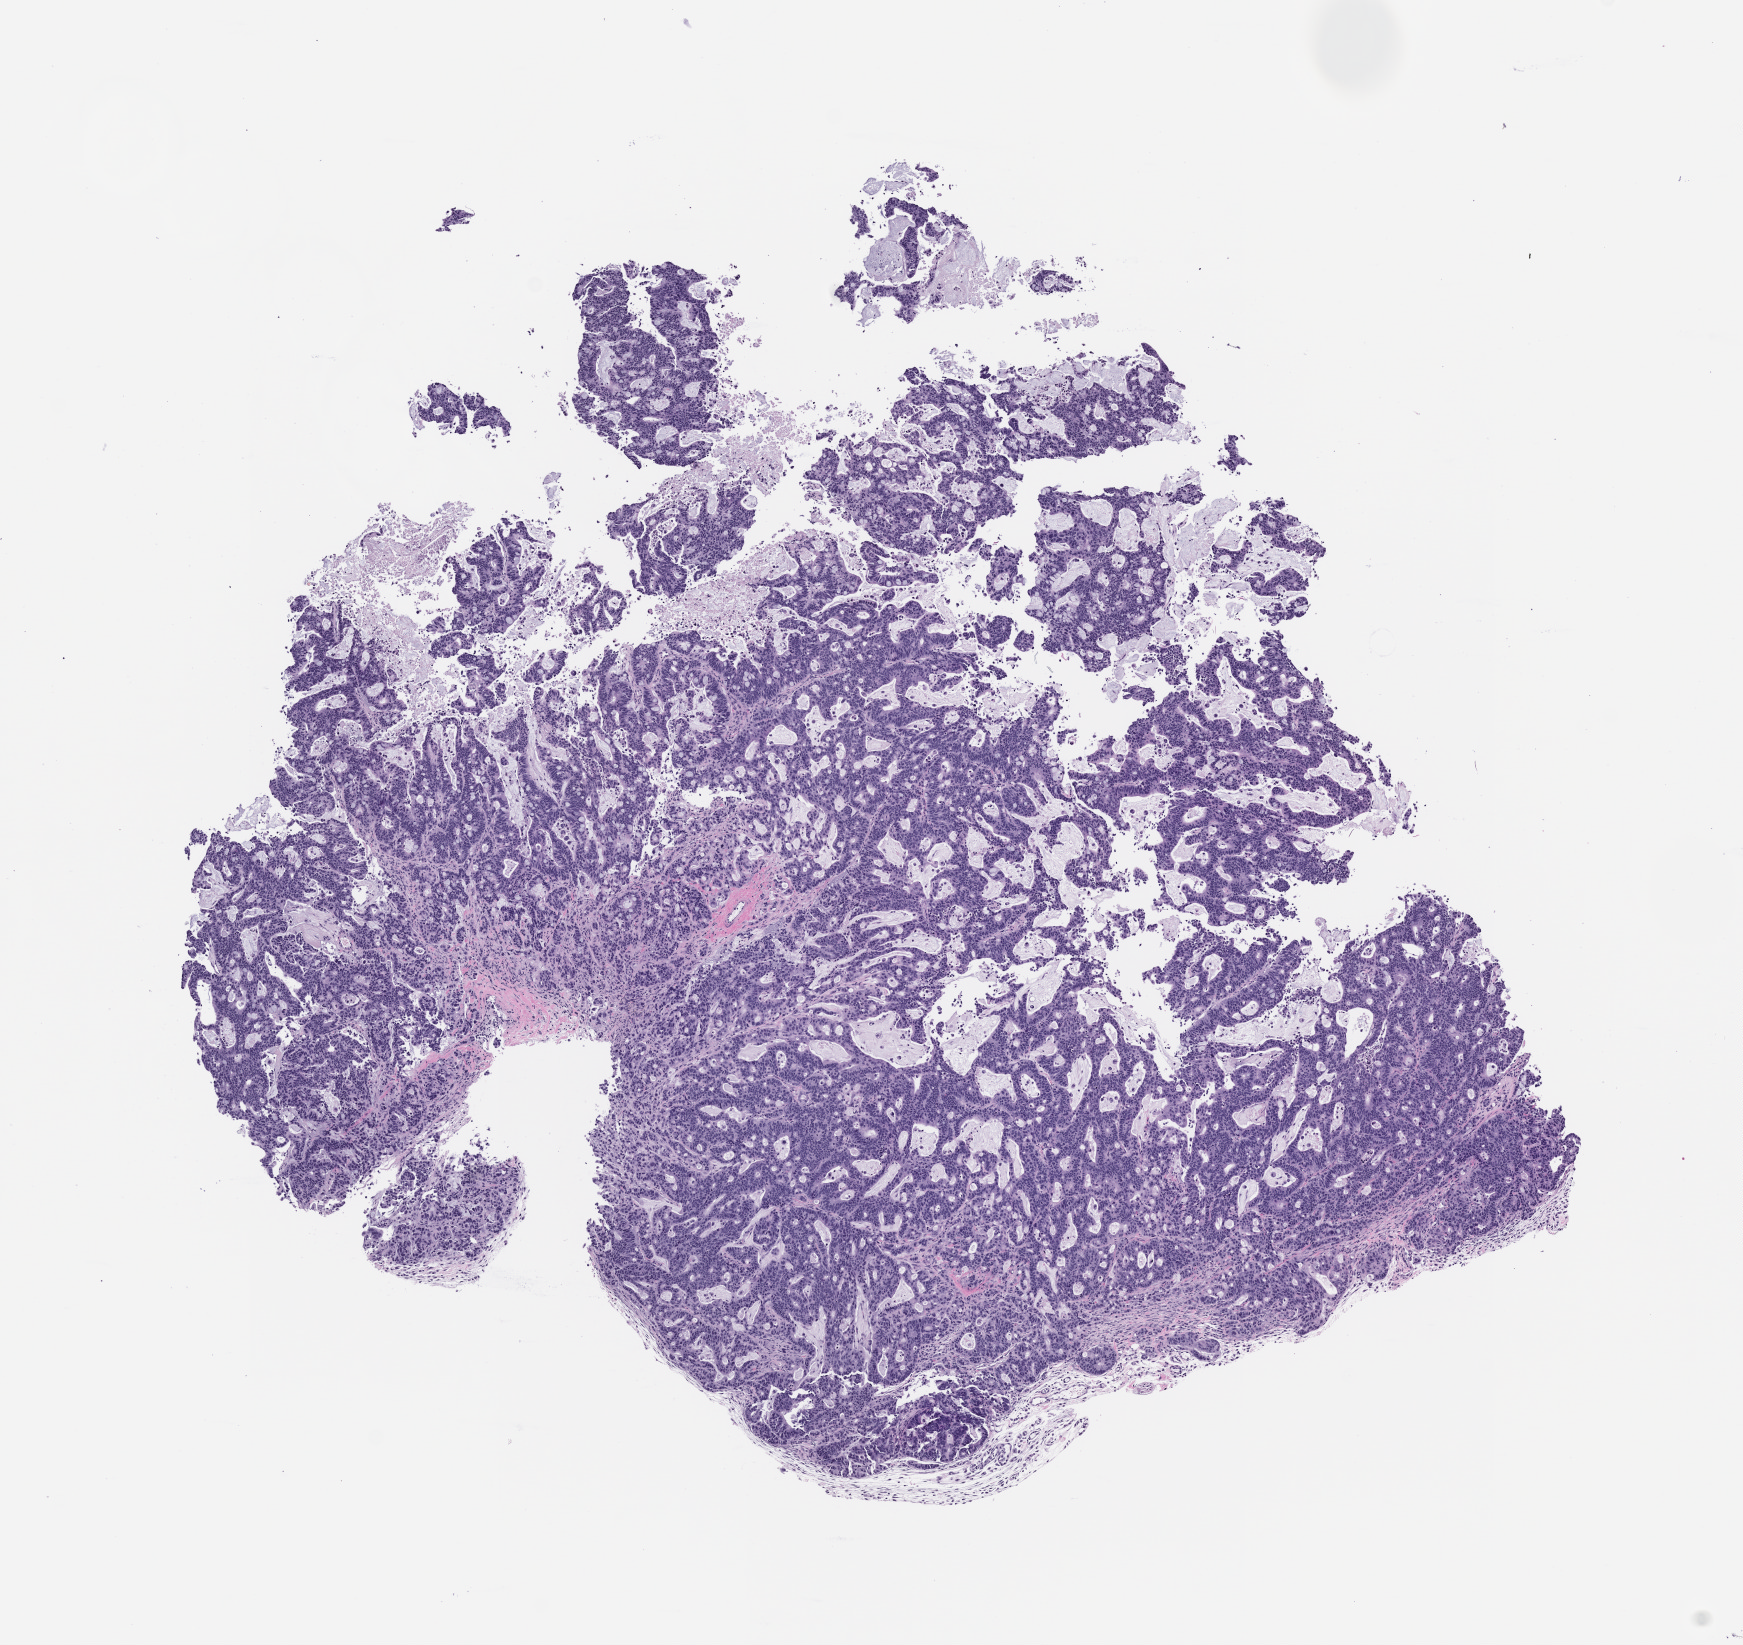
H&E whole-slide image of a patient-derived xenograft (PDX) tumor grown in a mouse, passage 0, shown as a low-resolution overview of the whole scanned area (about 7.0 x 6.6 mm). Formalin-fixed paraffin-embedded section. Originating tumor site category: rectum.
* originating patient diagnosis: Rectal Adenocarcinoma